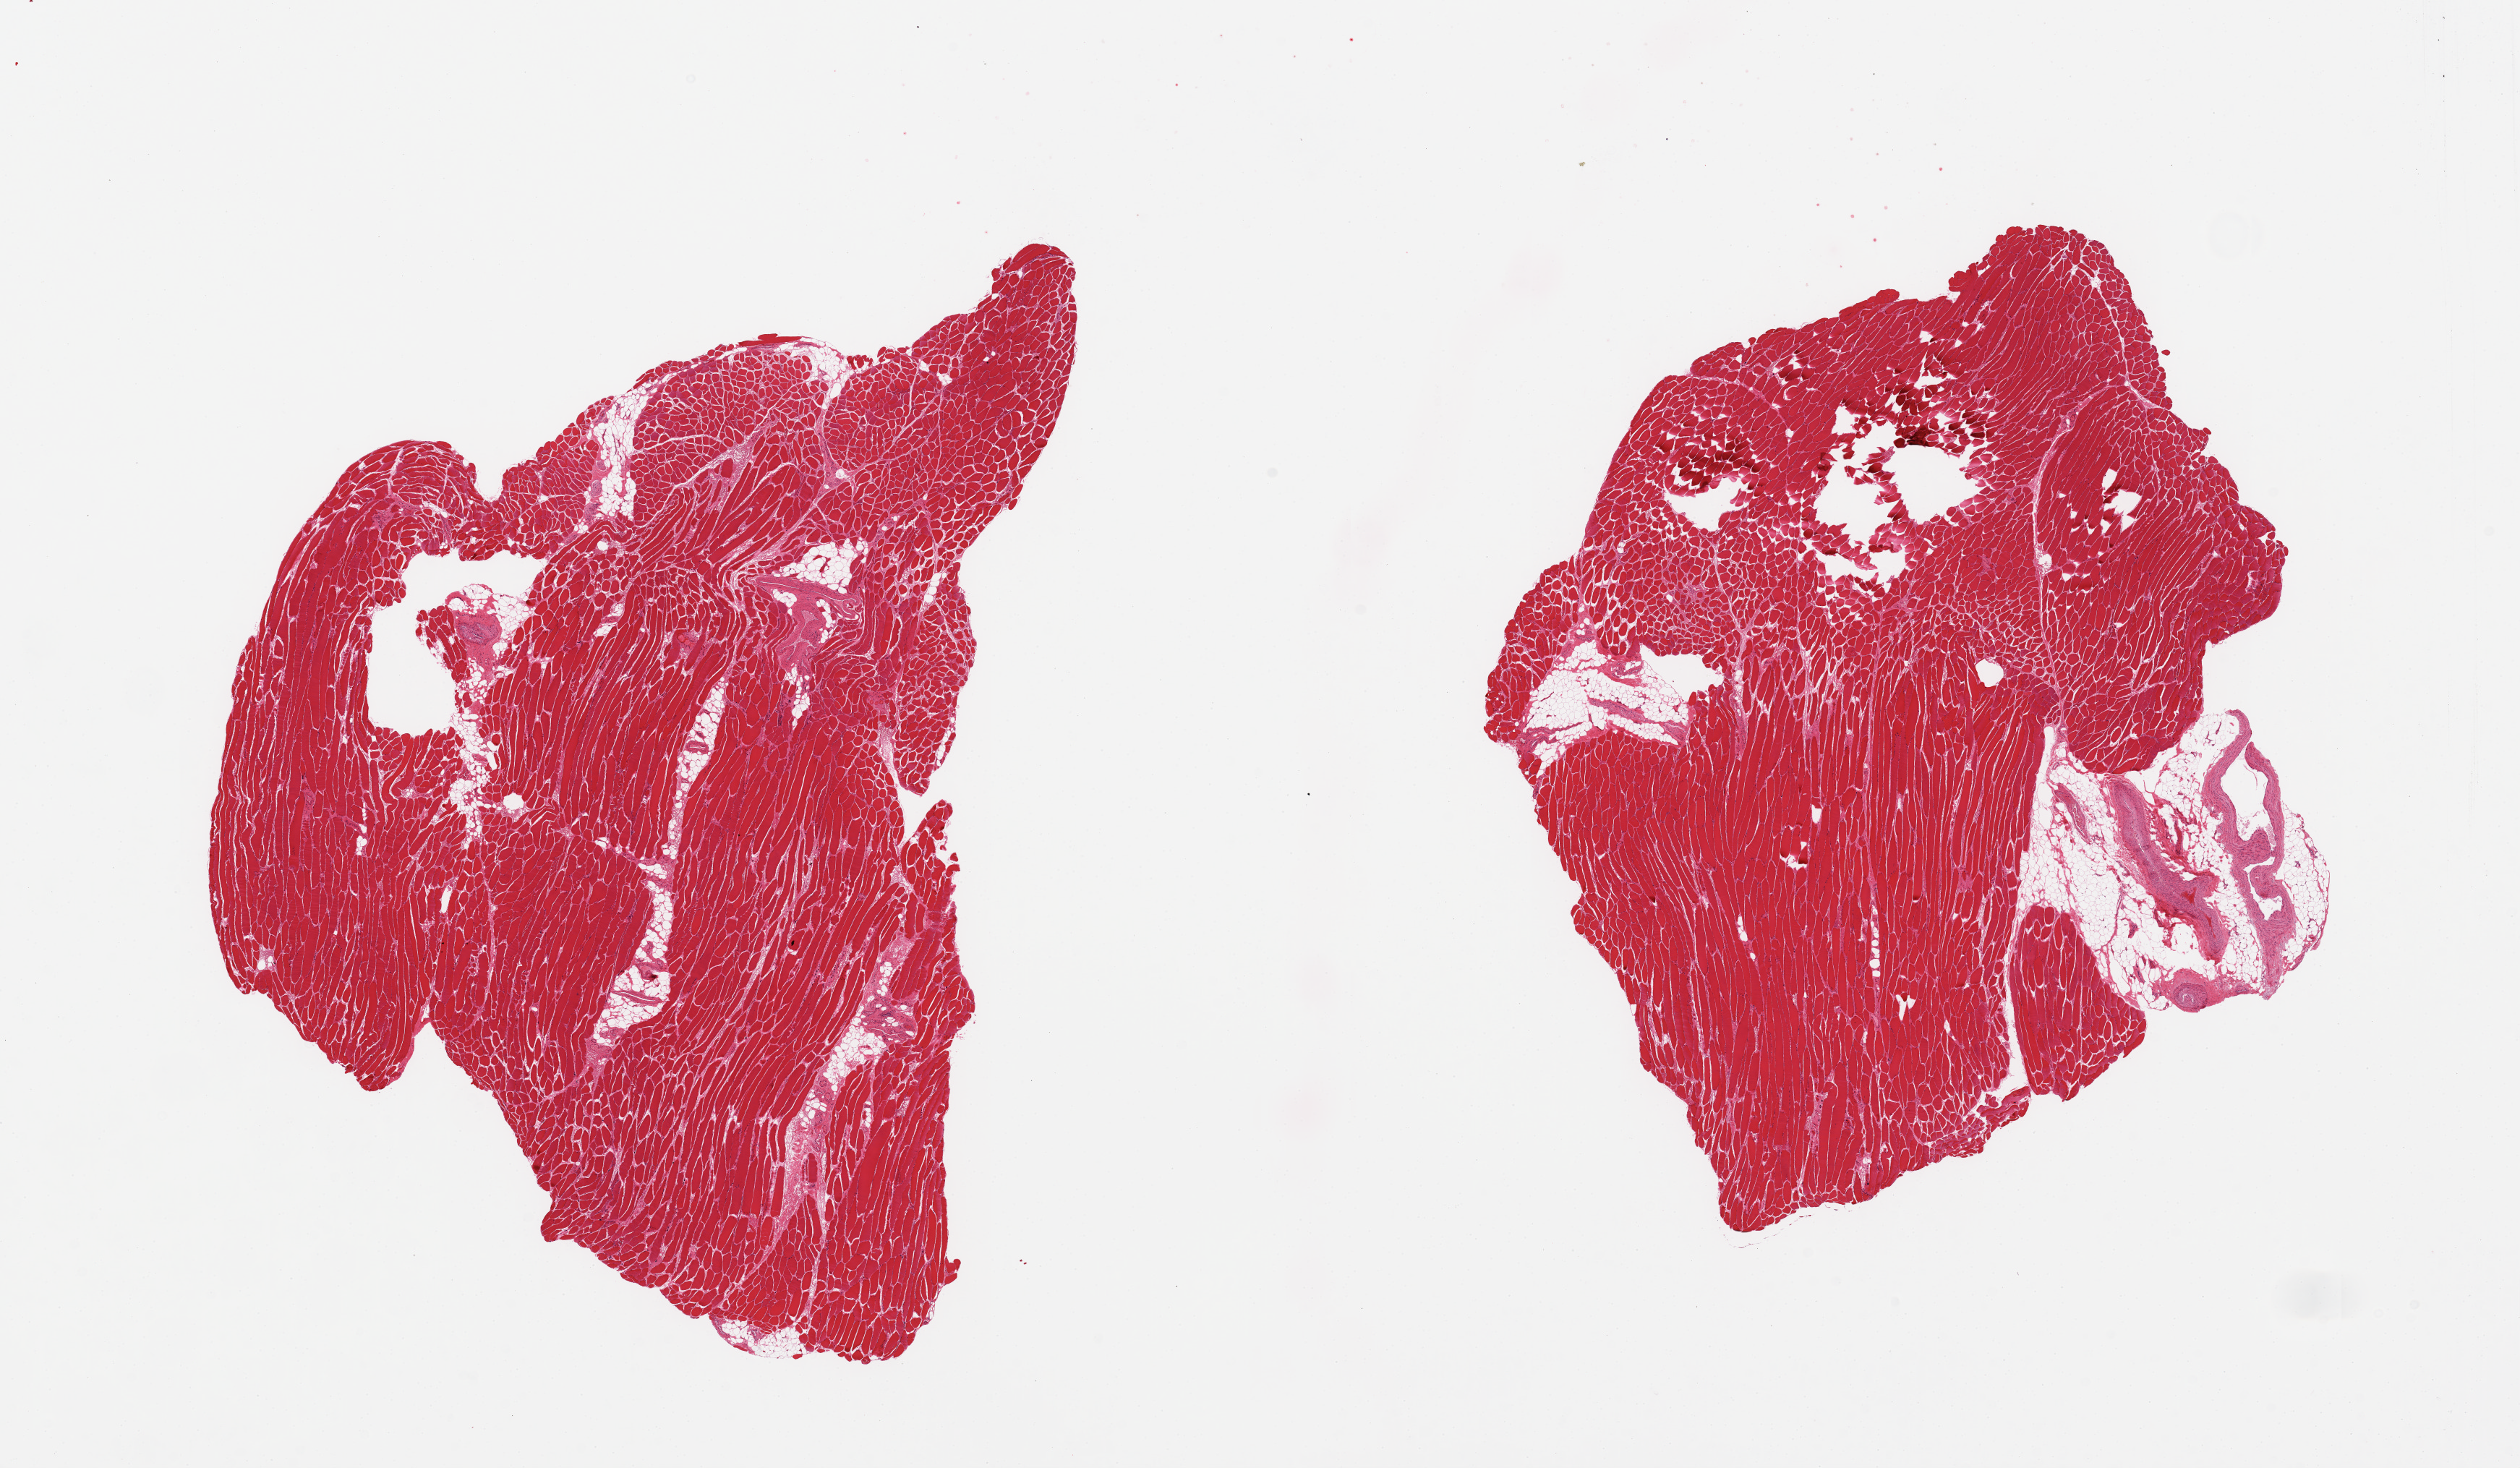
Digitized haematoxylin and eosin-stained section, shown as a low-resolution overview of the whole scanned area (about 27.6 x 16.1 mm); PAXgene-fixed paraffin-embedded (PFPE) section; sampled site (target tissue): skeletal muscle; tissue donor sample. Donor sex: male.
Review note (as recorded): 2 pieces, 5% internal fat, one piece has attachment of 10% additional fat and vessels.